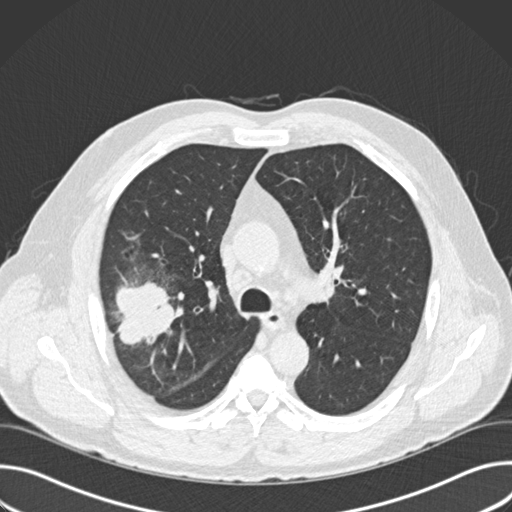
Low-dose screening chest CT, one axial slice. Position 108 of 157 along the scan axis. Lung window (W 1500 / L -600 HU). 512 × 512 image matrix, field of view 380 × 380 mm.
Outlined on this slice (expert manual segmentation):
- lesion 1 (tumor, upper lobe of right lung): bounding box <116,281,176,345> (left, top, right, bottom; pixels)